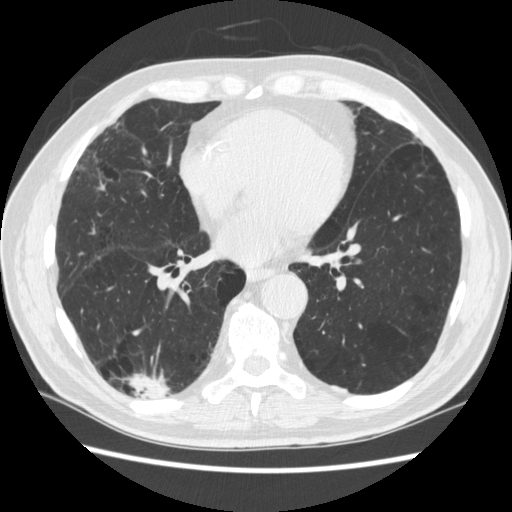
Low-dose screening chest CT, axial slice. Third screening round (two years after baseline). Lung window (W 1500 / L -600 HU). 1.25 mm slice thickness. Standard (soft-tissue) reconstruction kernel (STANDARD). 512 × 512 image matrix. Male participant, aged 70 years at enrolment. Former smoker at enrolment.
Expert reader's lesion annotation, bounding box [x1, y1, x2, y2] px = [125, 360, 181, 417]. The screening reader recorded 4 non-calcified nodules or masses ≥4 mm on this exam (right lower lobe, right lower lobe, left lower lobe, left lower lobe); which of them this box marks is not recorded. Official screen result: positive, other. Participant outcome: lung cancer diagnosed 253 days after this screen — squamous cell carcinoma, NOS, right upper lobe, poorly differentiated (G3), stage IV (AJCC 6th edition).